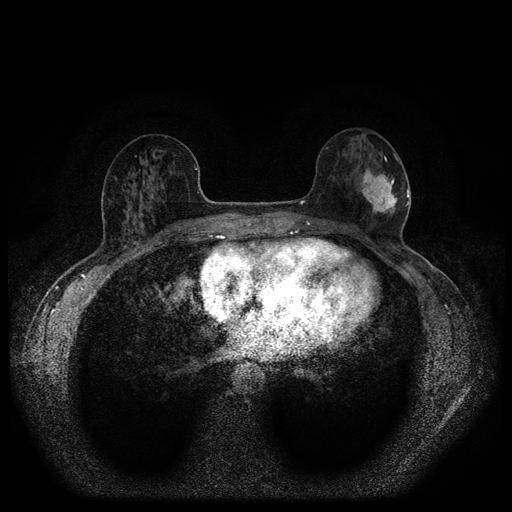
Breast MRI (dynamic contrast-enhanced, multi-phase), one axial slice; dynamic contrast-enhanced series, time point 2 of 5 at this slice position (early post-contrast); 1.5 T; TE 2.7 ms, TR 5.4 ms; 512 × 512 image matrix, field of view 330 × 330 mm. Female patient, age 56 years.
Structures marked on this image (semi-automatic segmentation, software-assisted and operator-edited):
- breast lesion (labelled 'tumour' in the annotation; benign lesions carry a separate 'benign' label): bounding box [x1, y1, x2, y2] px = [357, 168, 401, 220]